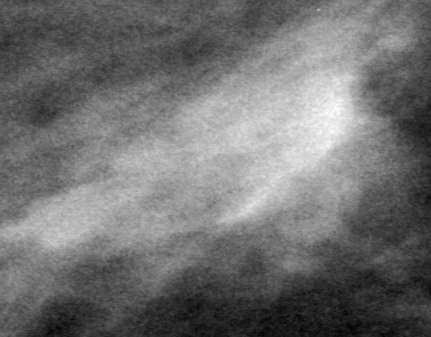
Region of interest cut from a scanned film mammogram (one marked finding); right breast; MLO view.
Mass, shape irregular, margins obscured; BI-RADS assessment category 0 (incomplete: needs additional imaging); pathology result (as recorded, not read from the image): benign.